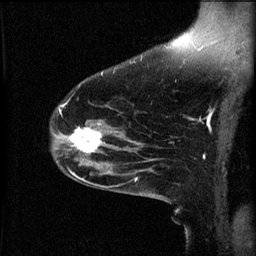
Breast MRI (dynamic contrast-enhanced), one sagittal slice. Position 39 of 60 along the scan axis. 3 images stored at this slice position (order not interpretable as contrast timing). 1.5 T. TE 4.2 ms, TR 8.2 ms. 2 mm slice thickness. 256 × 256 image matrix, field of view 200 × 200 mm. Female patient, age 49 years.
Outlined on this slice (semi-automatically segmented with operator editing):
- analysis volume of interest (the breast-tissue region the enhancement analysis was run in; not a lesion): bounding box <66,124,113,159> (left, top, right, bottom; pixels)
- tumour enhancement mask (voxels above the 70 % enhancement threshold inside the analysis volume of interest): <70,124,105,155>